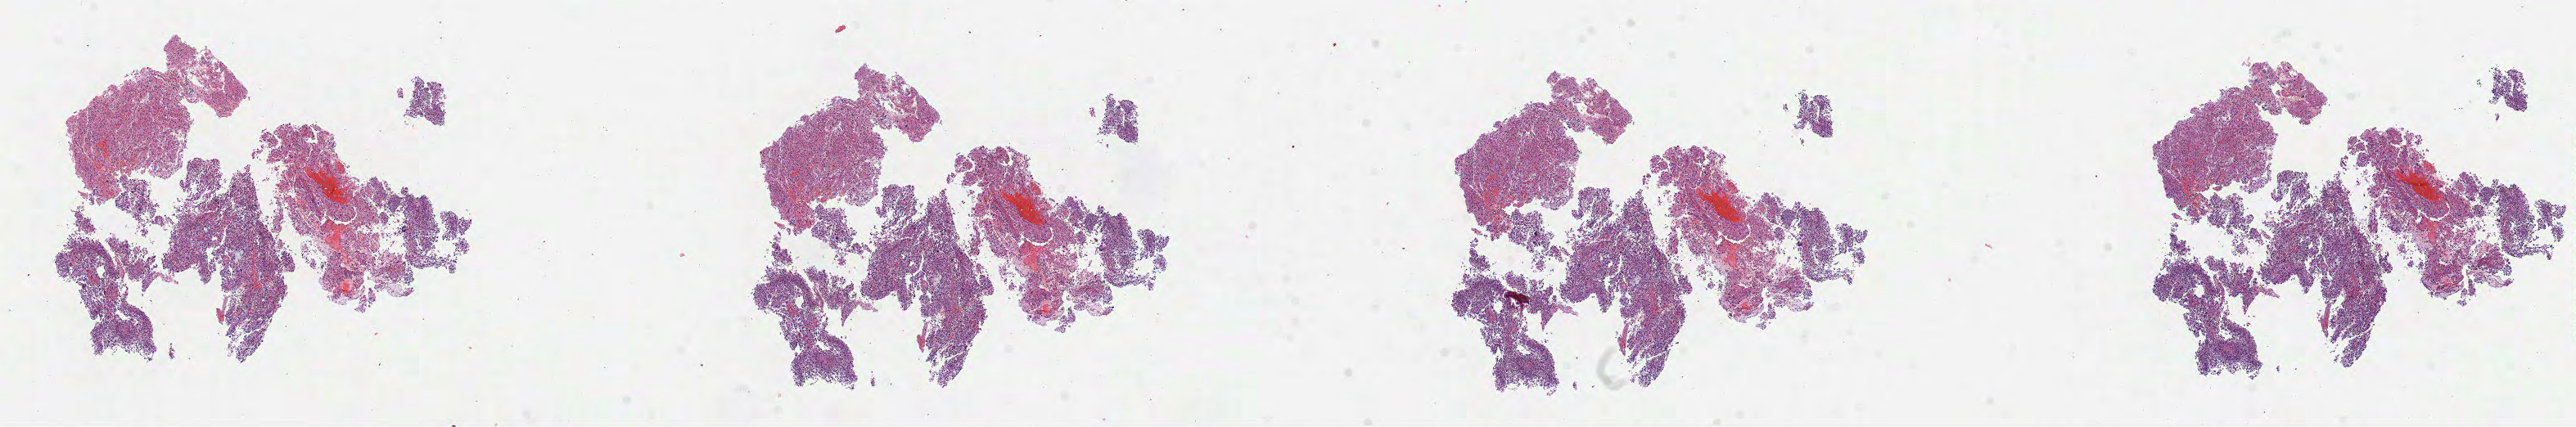
H&E-stained whole-slide image — a low-resolution overview of the entire scanned area, about 25.4 x 4.2 mm, FFPE section, primary tumour sample from the brain. Female, age 23 years at initial diagnosis.
Pathologic diagnosis: Glioblastoma.